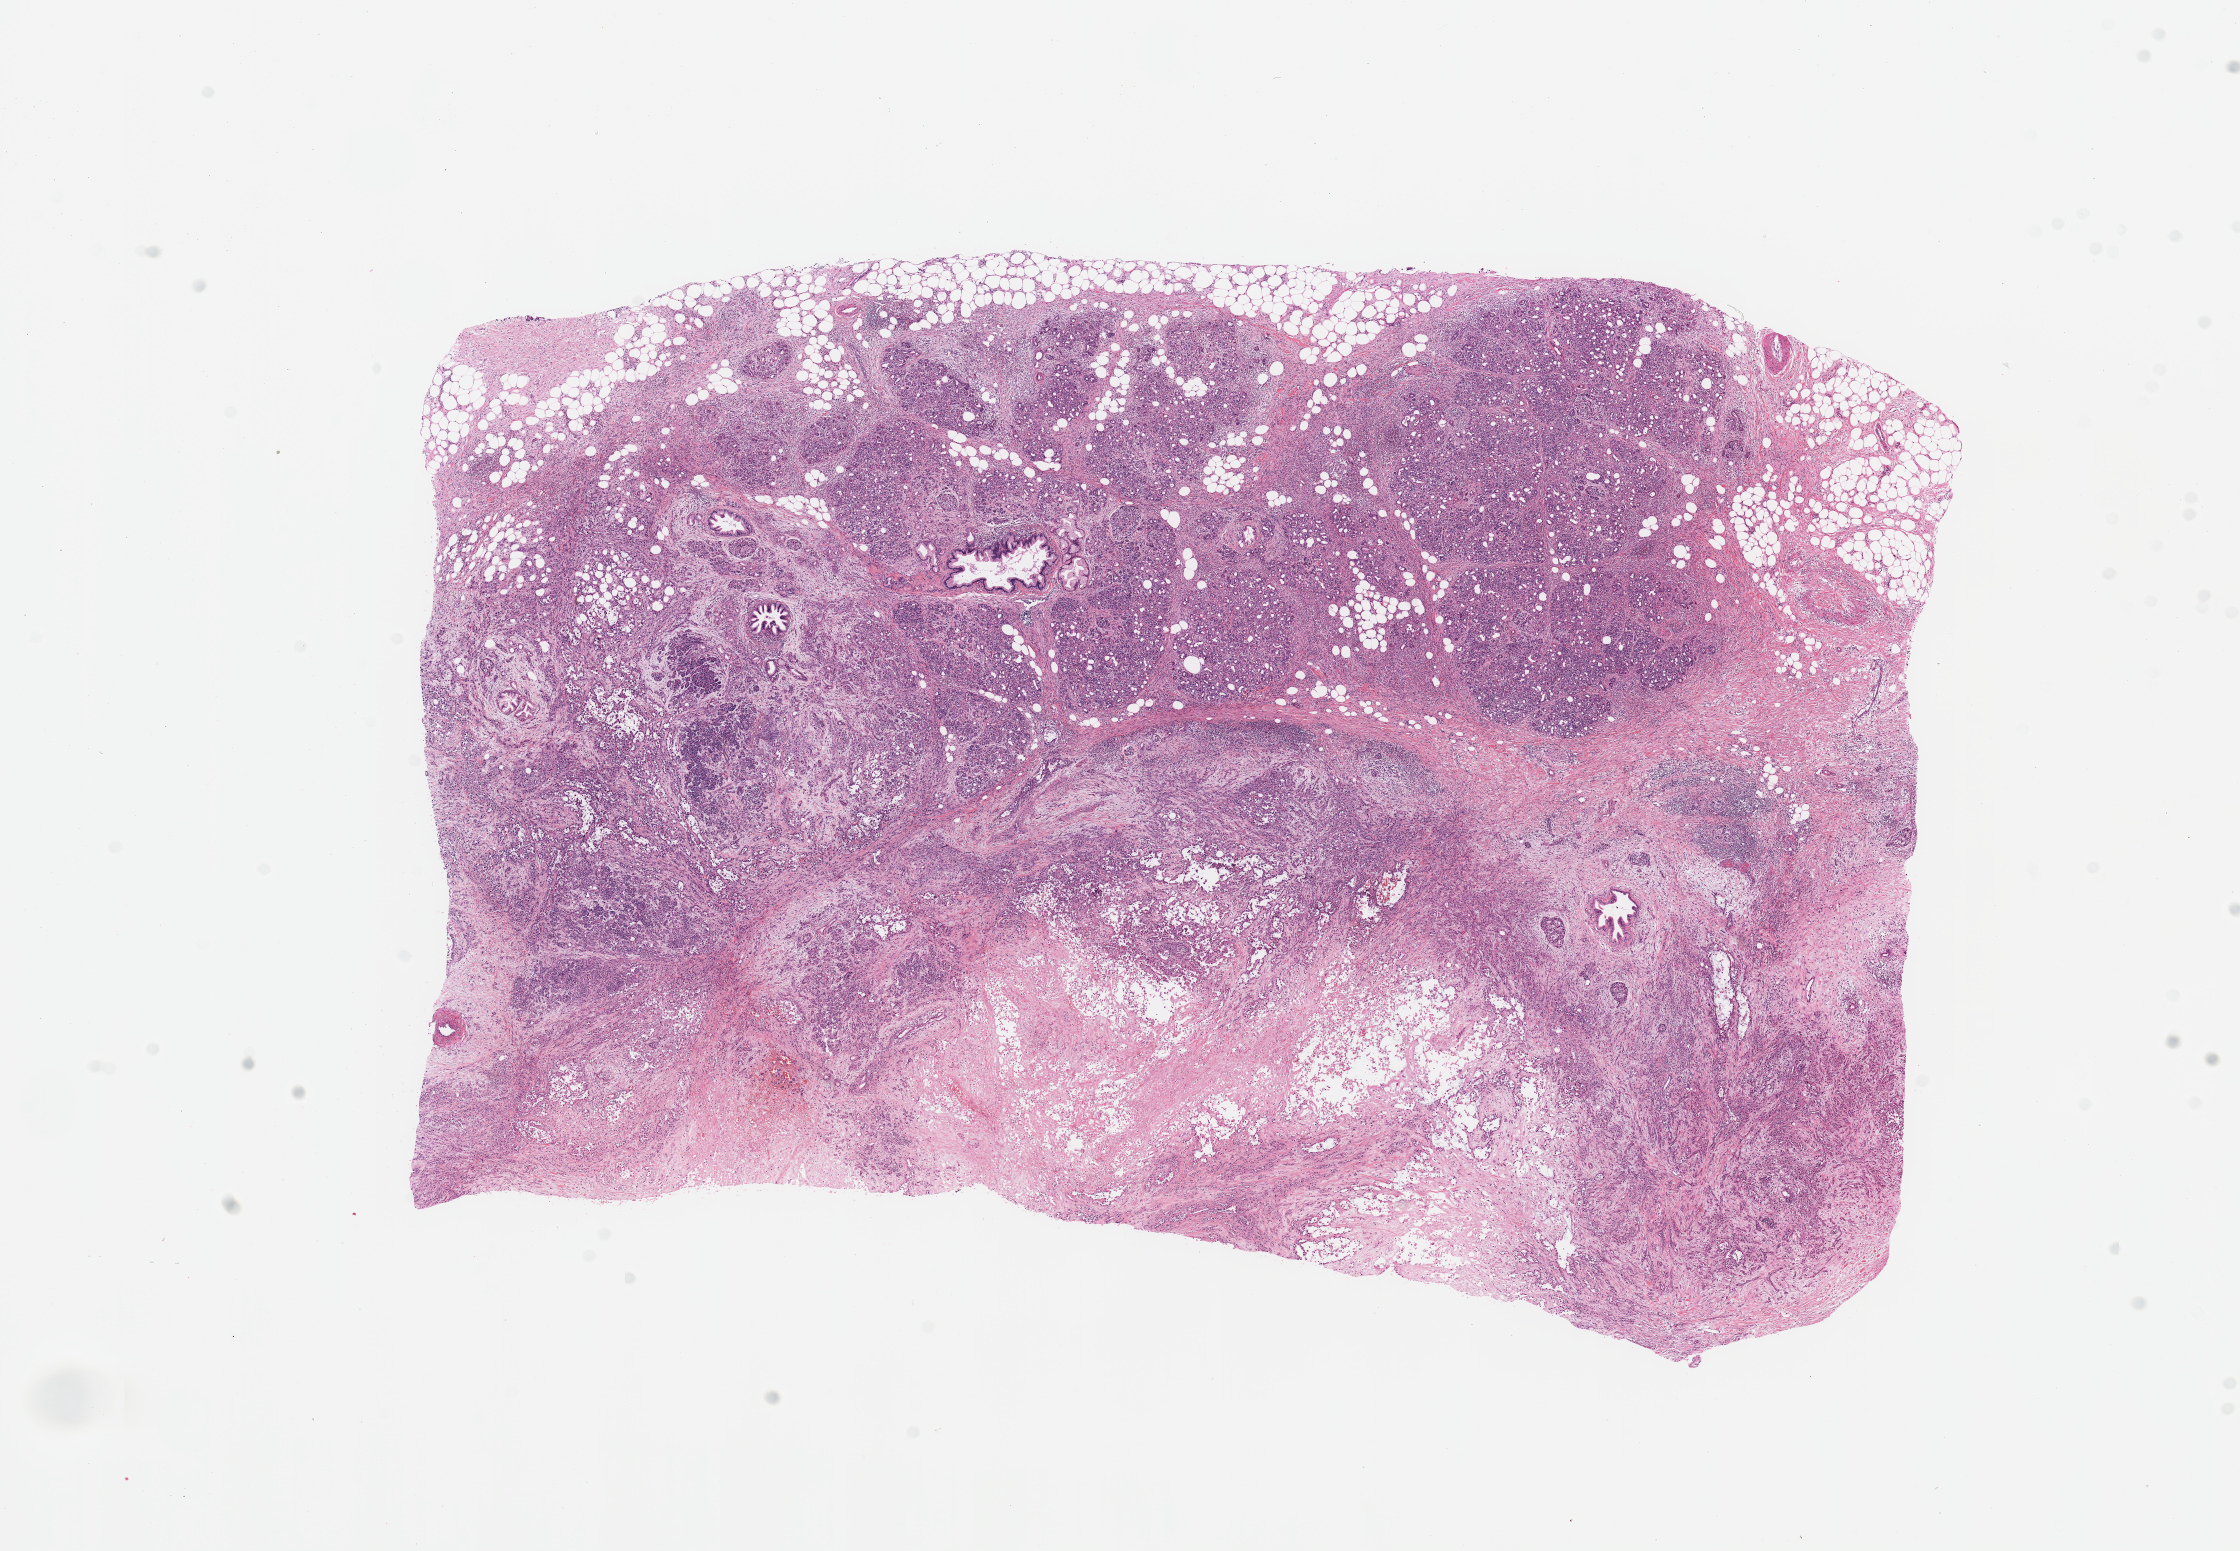
H&E-stained whole-slide image — a low-resolution overview of the entire scanned area, about 17.7 x 12.3 mm (slide scanned at 20x). Tumour tissue sample, sampled site: pancreas. Female, 60 y/o. Histologic grade: G3 (poorly differentiated). Slide review estimates, as recorded: tumour nuclei 20%, necrosis 10%.
* primary tumour site (as recorded): head
* AJCC pathologic stage: IIB
* diagnosis: Infiltrating duct carcinoma, NOS